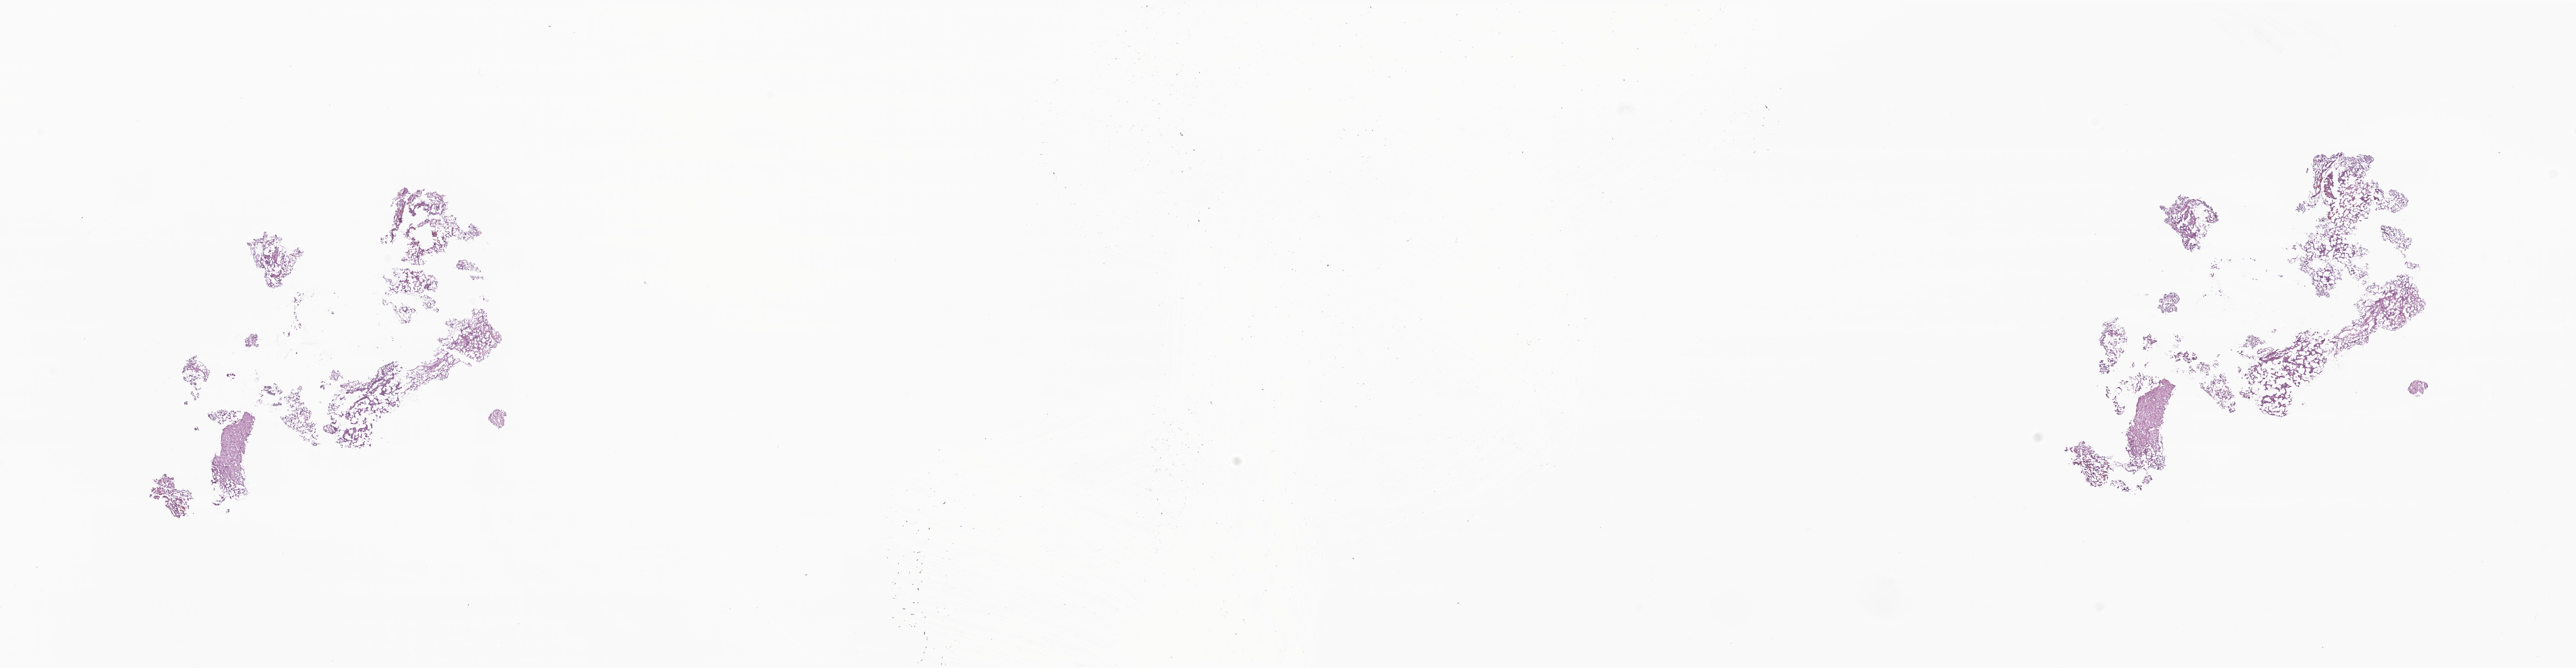
Whole-slide image, haematoxylin and eosin stain of tumor tissue from the brain — shown as a low-resolution overview of the whole scanned area (about 31.6 x 8.2 mm); frozen section. Patient male; age 434 days (about 1.2 years).
Diagnosis (ICD-O-3 morphology term): Atypical teratoid/rhabdoid tumor.